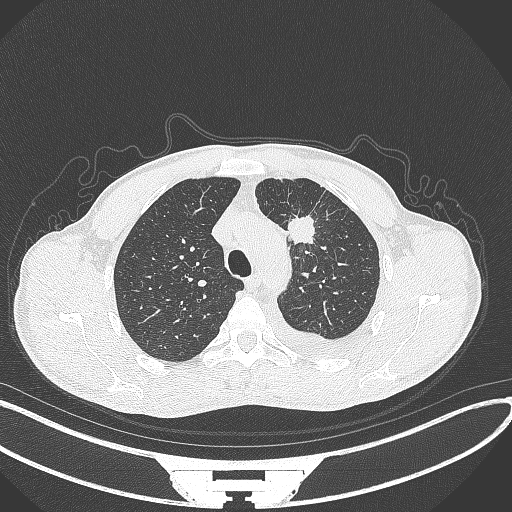
Chest CT, one axial slice; position 260 of 371 along the scan axis; reconstruction kernel B70f; 120 kVp; lung window (W 1500 / L -600 HU); 1 mm slice thickness; 512 × 512 image matrix, field of view 400 × 400 mm. Male patient, age 49 years. Case-level facts recorded for this patient, not image findings: clinical TNM (as recorded): T1c N1 M1.
Annotated regions visible in this slice (rectangle marked by the reading radiologist):
- lung tumour (recorded histology: adenocarcinoma): bounding box [x1, y1, x2, y2] px = [287, 215, 319, 250]